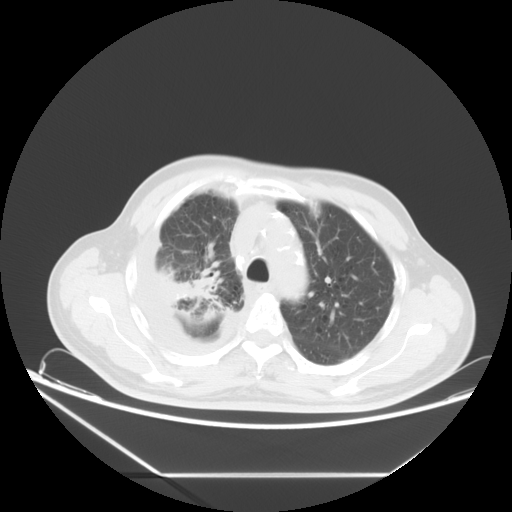
Chest CT, one axial slice; position 11 of 16 along the scan axis; reconstruction kernel STANDARD; lung window (W 1500 / L -600 HU); 5 mm slice thickness; 512 × 512 image matrix, field of view 418 × 418 mm. Male patient, age 75 years. From the clinical record (not read from this slice): clinical TNM (as recorded): T1c N1 M1.
Outlined on this slice (rectangle marked by the reading radiologist):
- lung tumour (recorded histology: adenocarcinoma): bounding box <158,262,216,309> (left, top, right, bottom; pixels)